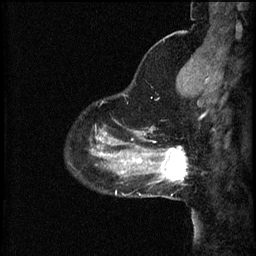
Breast MRI (dynamic contrast-enhanced), one sagittal slice. Slice 13 of 60 in the series (ordered by position). 3 images stored at this slice position (order not interpretable as contrast timing). 1.5 T. TE 4.2 ms, TR 8.2 ms. 256 × 256 image matrix, field of view 200 × 200 mm. Patient: female, 37 years.
Structures marked on this image (semi-automatic segmentation, software-assisted and operator-edited):
- analysis volume of interest (the breast-tissue region the enhancement analysis was run in; not a lesion): bounding box [x1, y1, x2, y2] px = [148, 140, 189, 181]
- tumour enhancement mask (voxels above the 70 % enhancement threshold inside the analysis volume of interest): [162, 148, 189, 181]